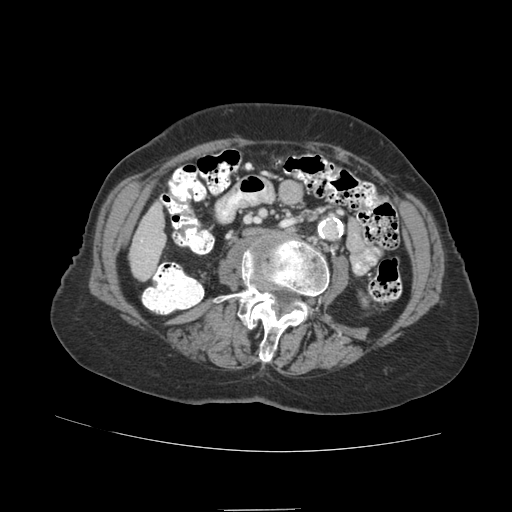
Contrast-enhanced abdominal CT (liver protocol), one axial slice. Reconstruction kernel STANDARD. Soft-tissue window (W 400 / L 40 HU). 2.5 mm slice thickness. 512 × 512 image matrix, field of view 360 × 360 mm. From the clinical record (not read from this slice): diagnosis: hepatocellular carcinoma (patient treated with transarterial chemoembolisation; whether this scan precedes or follows treatment is not stated here); TNM stage (as recorded): Stage-II; Child-Pugh class: A; tumour differentiation: moderately differentiated; tumour nodularity: multinodular.
Annotated regions visible in this slice (semi-automatically segmented with operator editing):
- liver parenchyma outside the tumour (the mass and vessels are separate outlines, so this box may not span the whole liver): bounding box (x1, y1, x2, y2) in pixels: (130, 202, 166, 280)
- liver vessels: (141, 240, 149, 251)